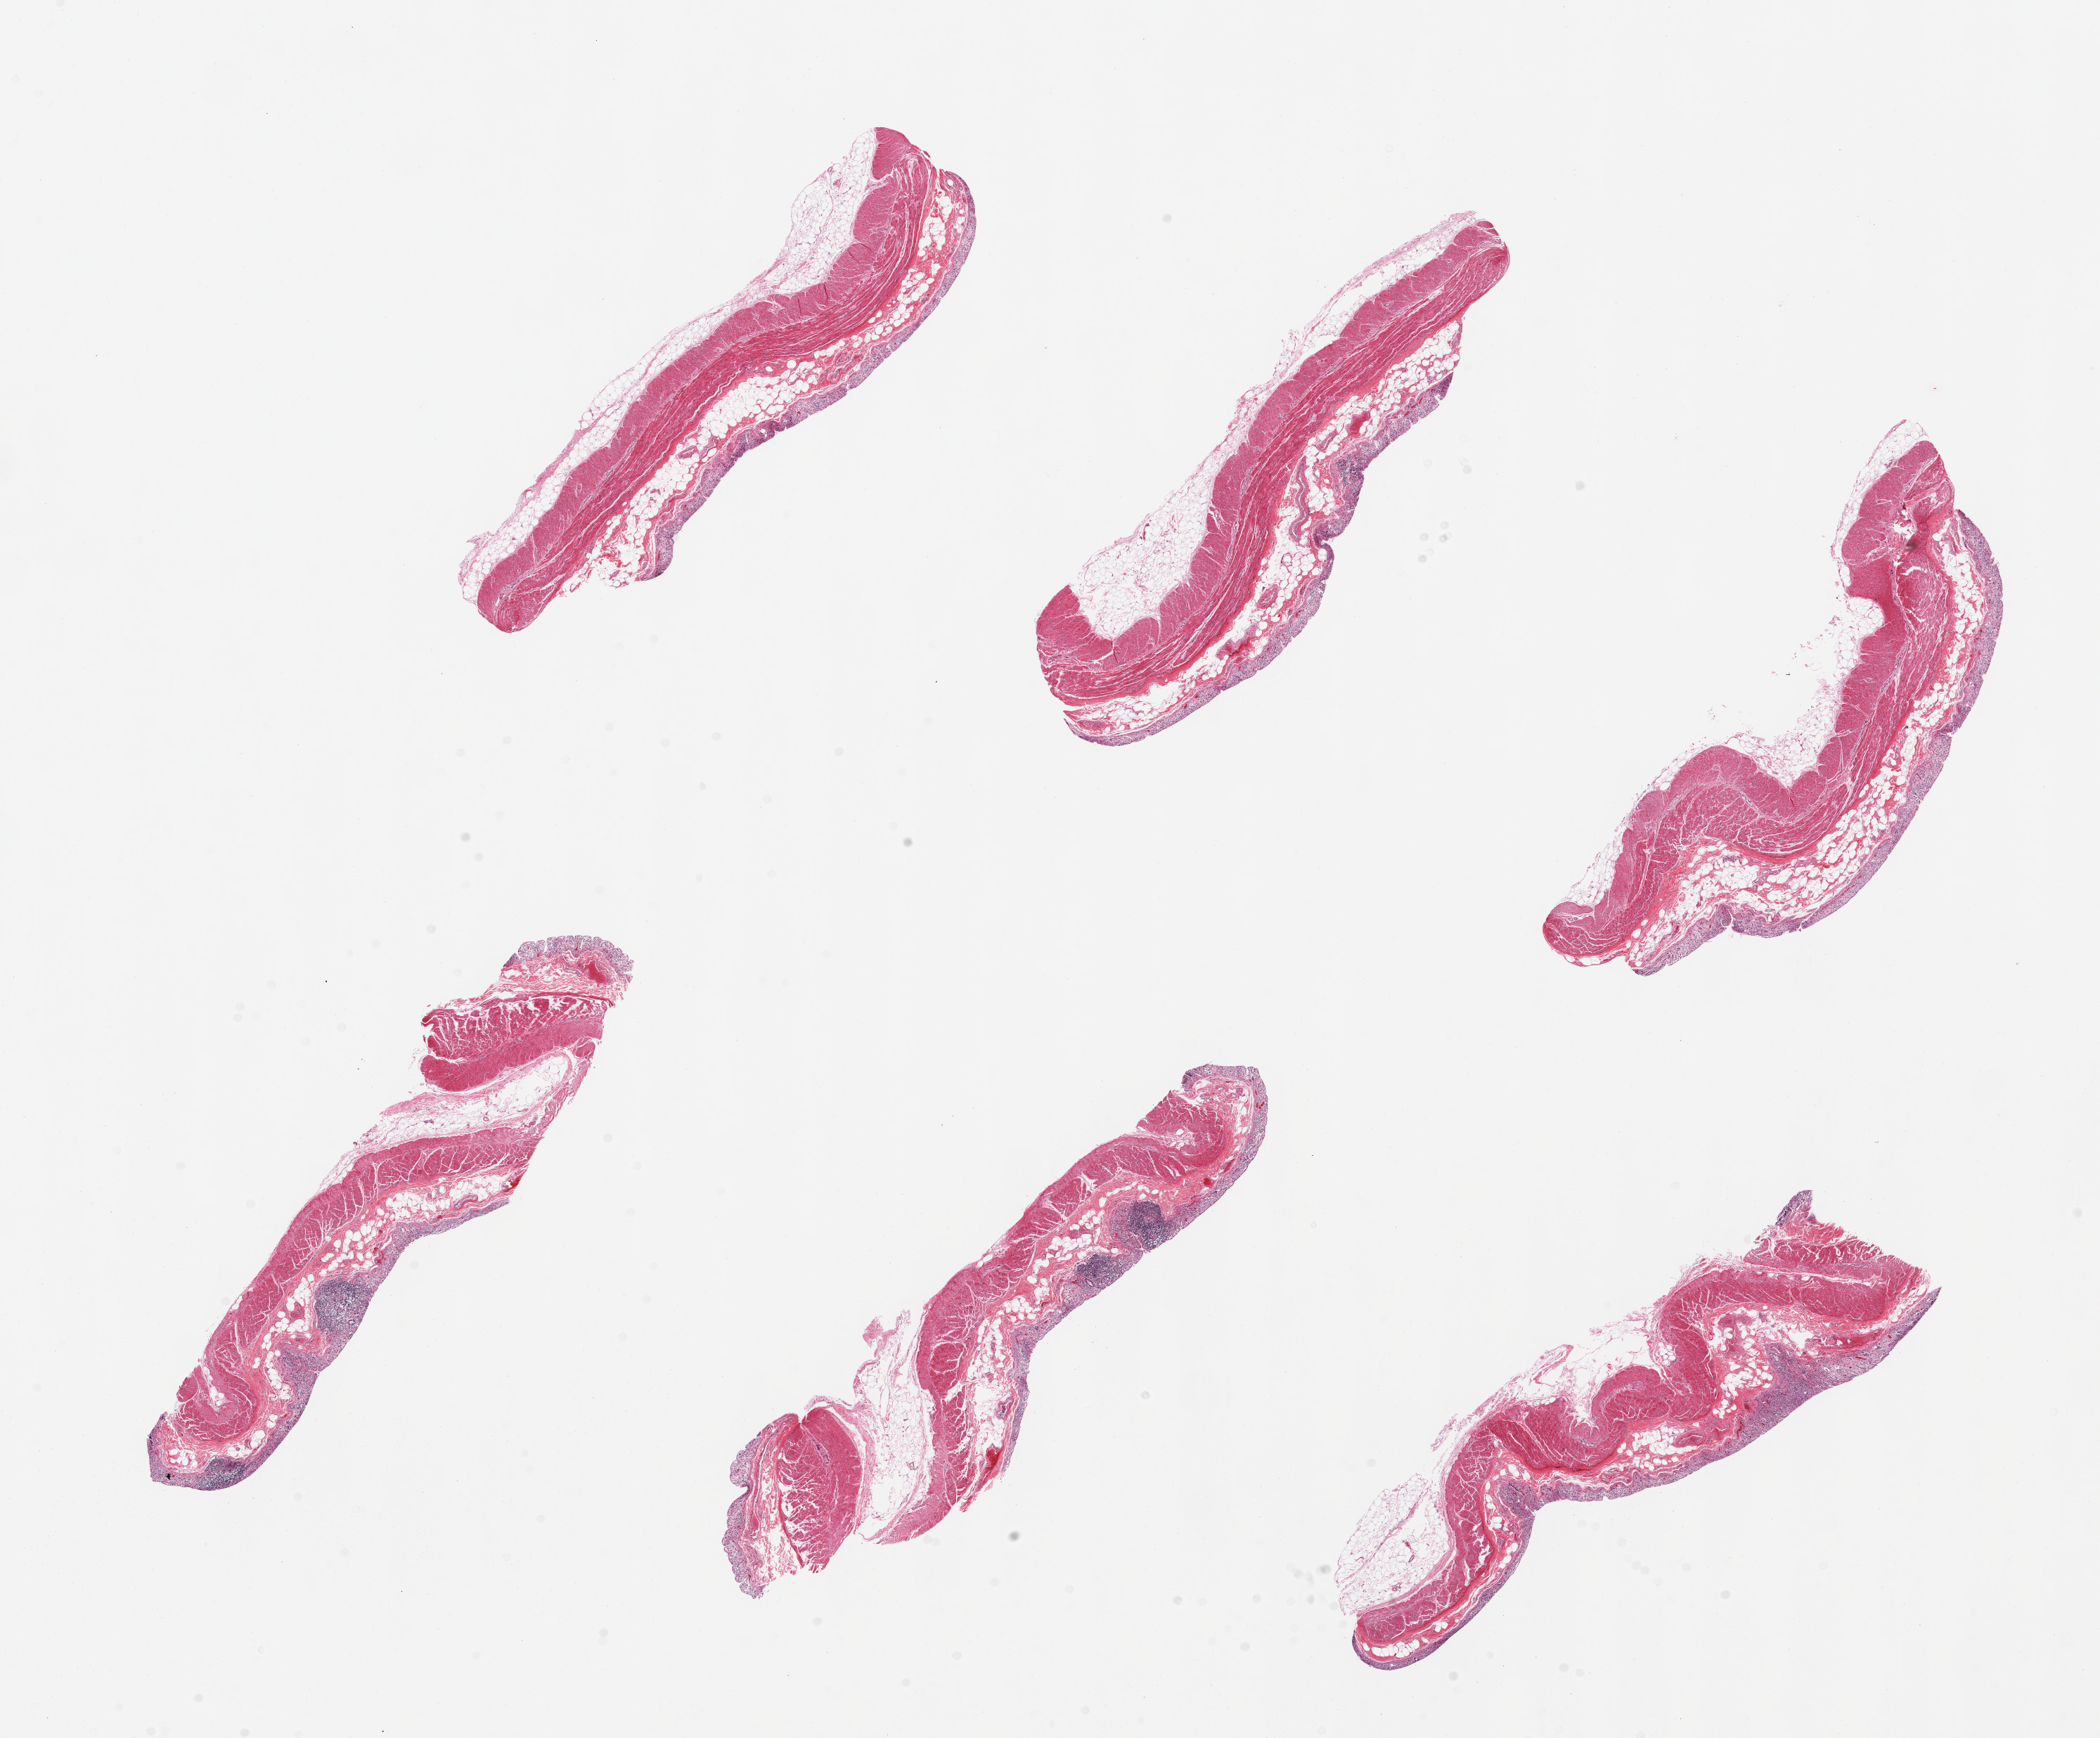
Haematoxylin and eosin whole-slide image, low-resolution overview of the scanned area, about 23.6 x 19.6 mm (acquisition: 20x scan), PAXgene-fixed paraffin-embedded (PFPE) section, target tissue: transverse colon, donor tissue sample.
Review note (as recorded): 6 pieces; mucosa is totally autolyzed, but muscularis is OK (1) as is mucosal lymphoid tissue.